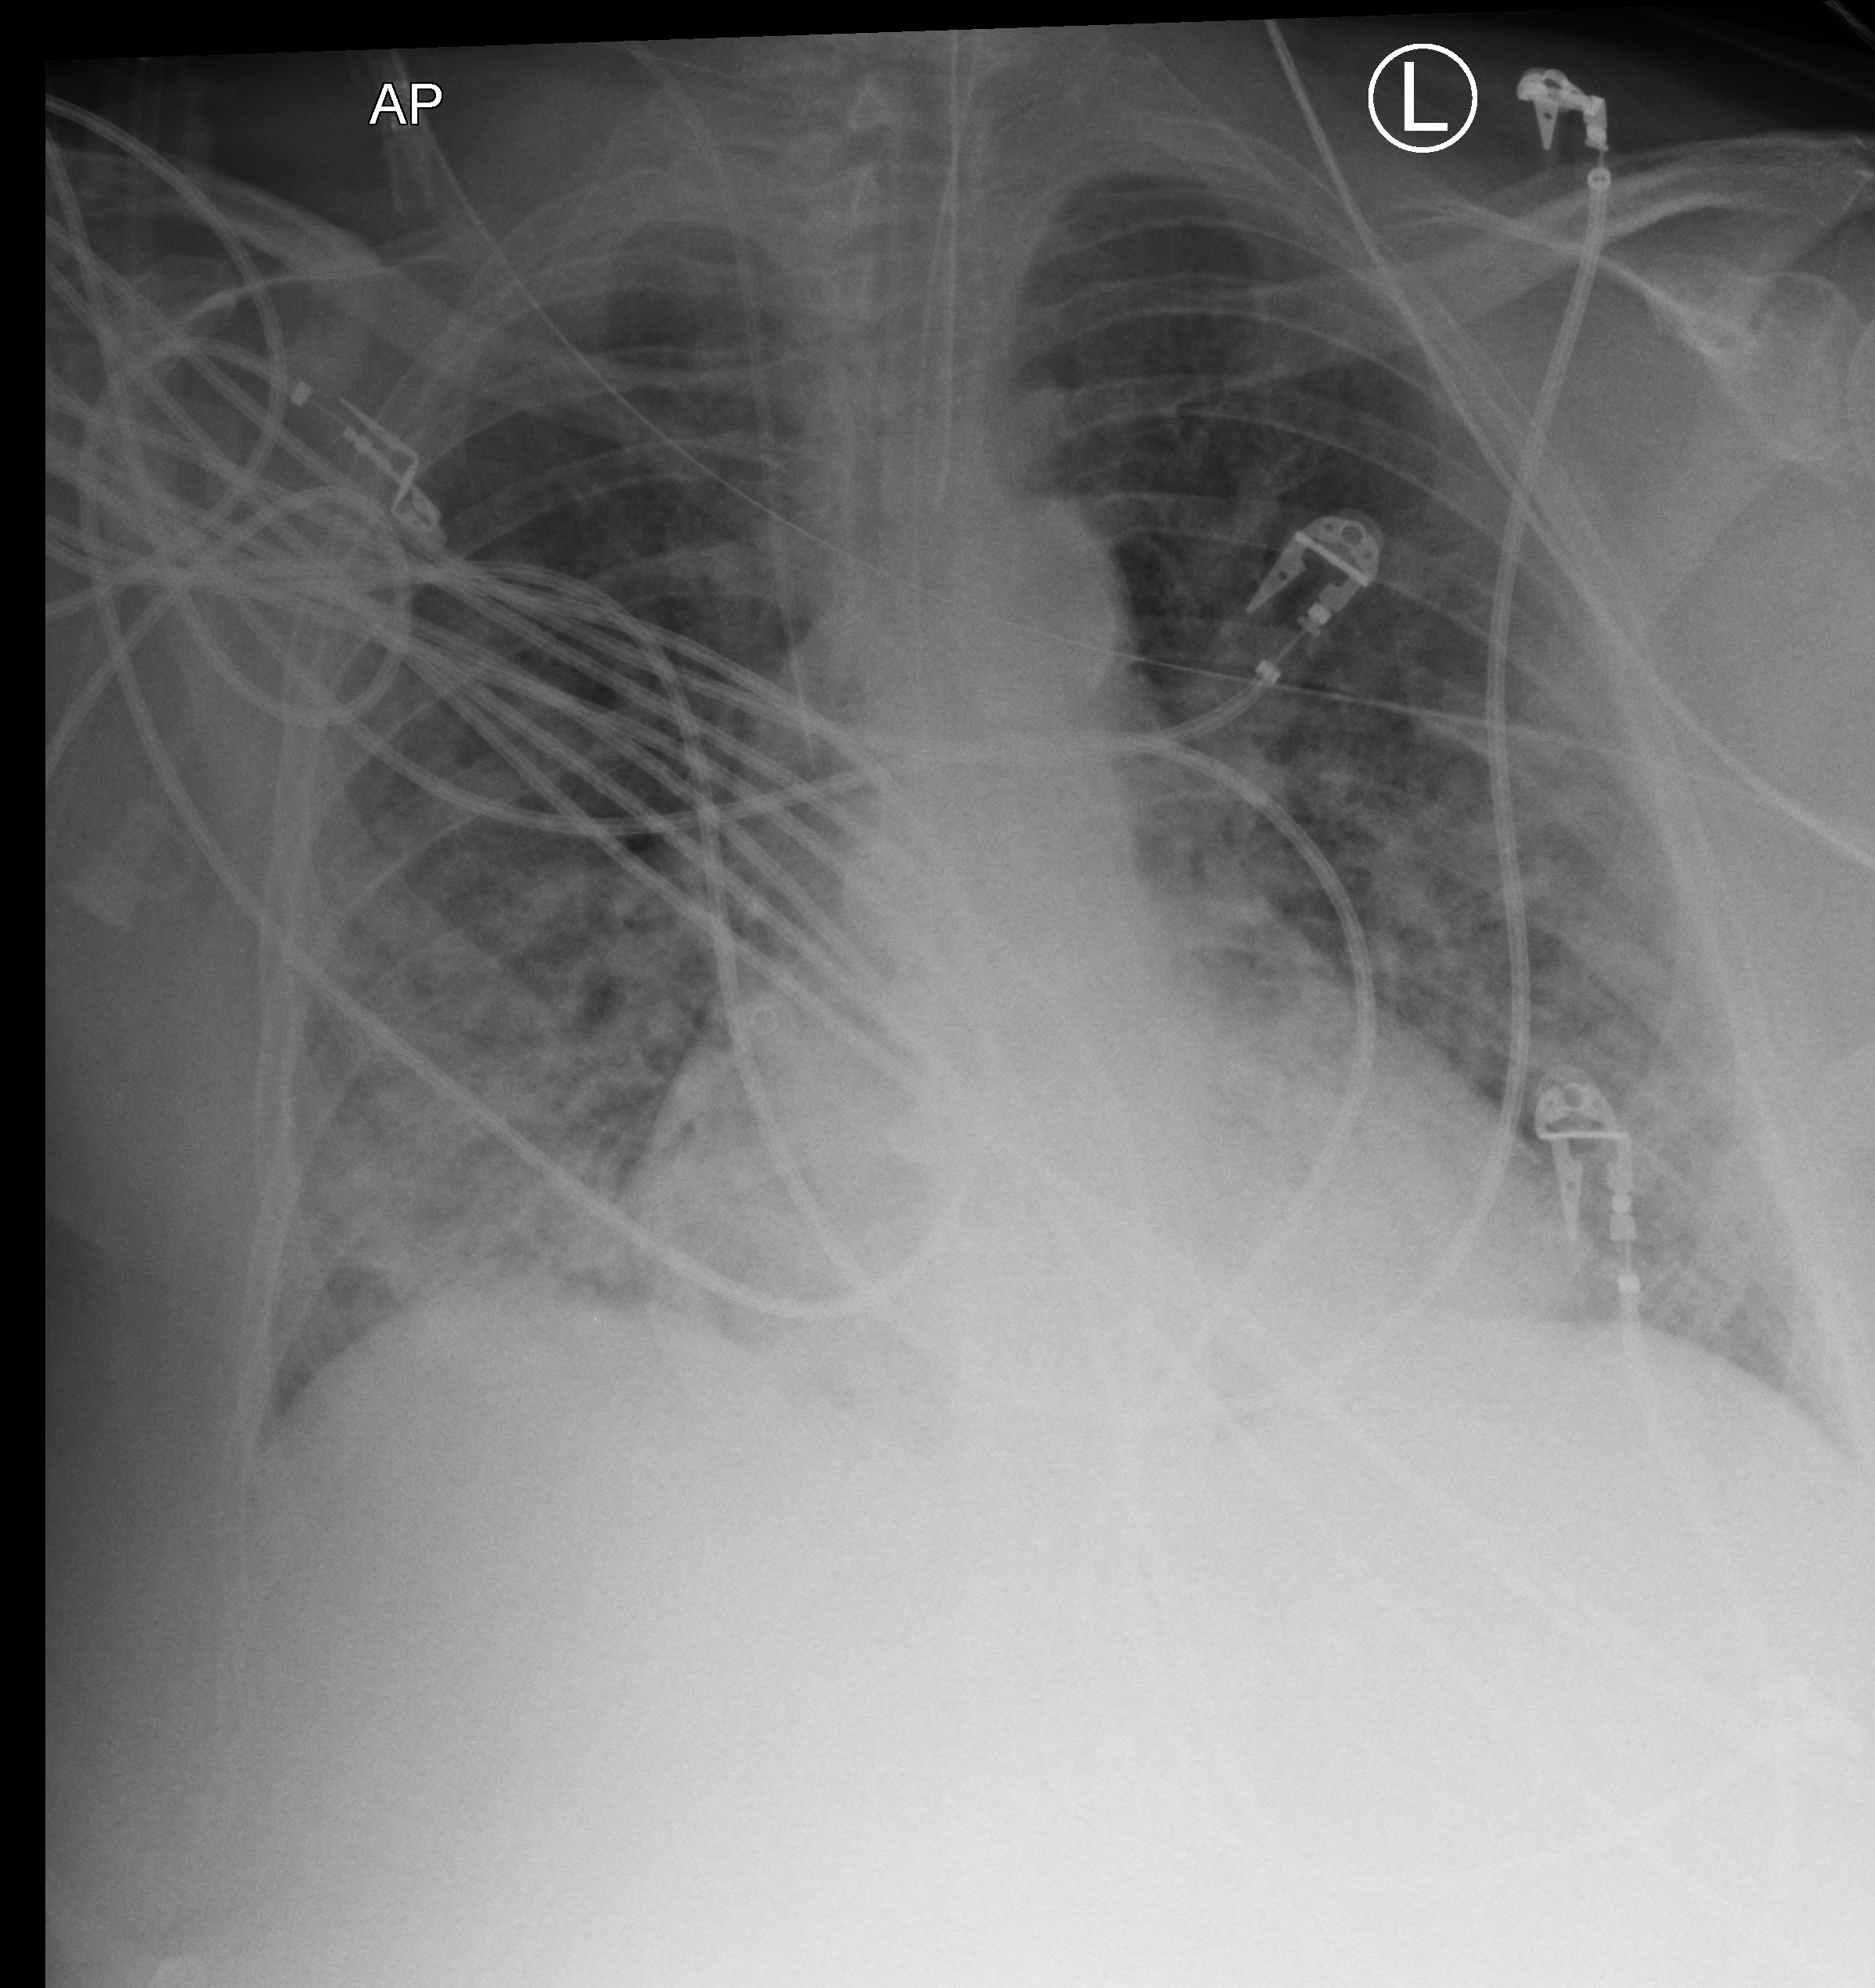
Portable chest radiograph. Patient hospitalised with COVID-19; female, aged 75–90 years.
From the hospital-stay record, not from the radiograph (when in the stay this image was taken is not recorded):
- admitted to intensive care during this hospital stay: yes
- mechanically ventilated during this hospital stay: yes